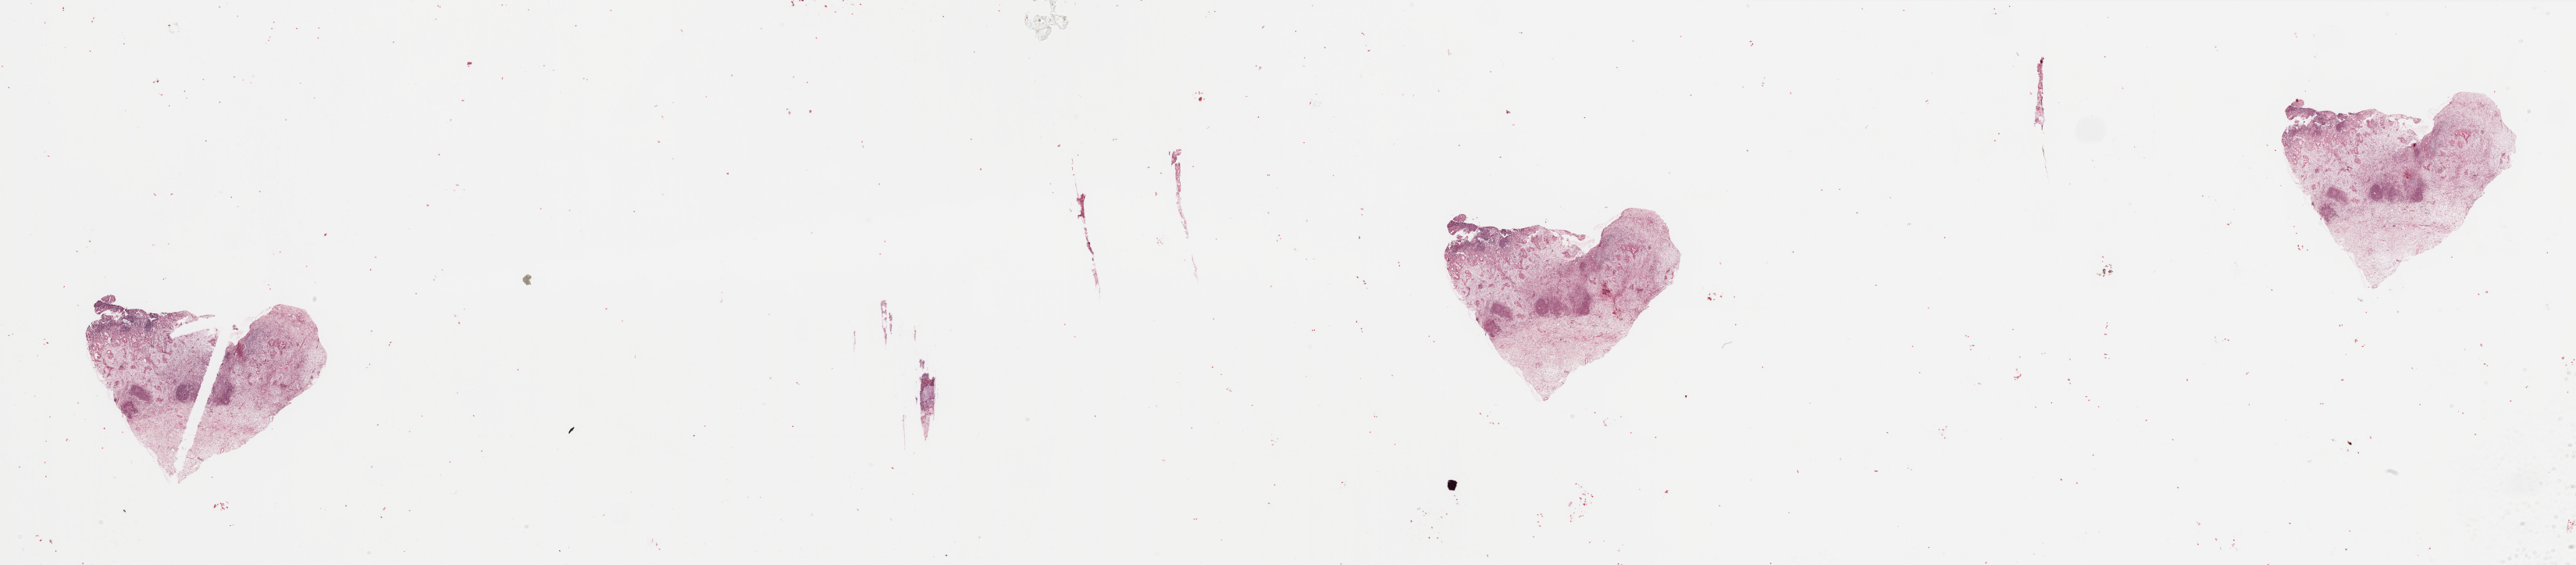
Digitized H&E-stained tissue section (whole slide) — whole scanned area (about 52.2 x 11.4 mm, slide scanned at 20x) shown as a low-resolution overview, tumour tissue sample, sampled site: pancreas. 63-year-old male patient. Histologic grade: G2 (moderately differentiated). Pathologist review of this section (percent, as recorded): tumour nuclei 20%, necrosis 0%.
Diagnosis: Infiltrating duct carcinoma, NOS. Primary tumour site (as recorded): head.